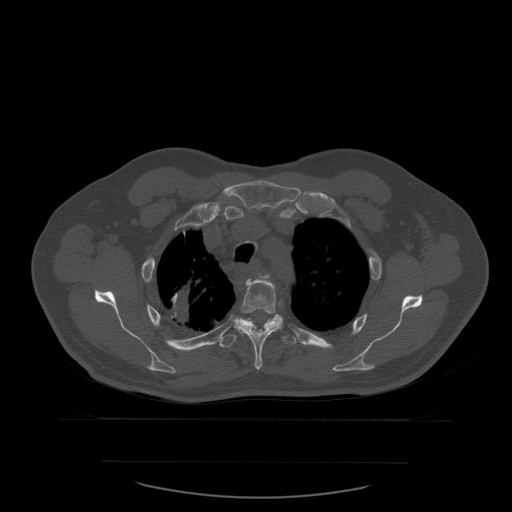
CT including the spine, one axial slice. Position 439 of 590 along the scan axis. Bone window (W 1800 / L 400 HU). 1.25 mm slice thickness. 512 × 512 image matrix, field of view 479 × 479 mm. Patient age 71 years. From the clinical record (not read from this slice): primary cancer: lung.
Outlined on this slice (semi-automatically segmented with operator editing):
- T3 vertebra: box from (x=267, y=276) to (x=270, y=279) px
- T4 vertebra: (x=234, y=274)–(x=284, y=370)
- T5 vertebra: (x=219, y=319)–(x=297, y=349)